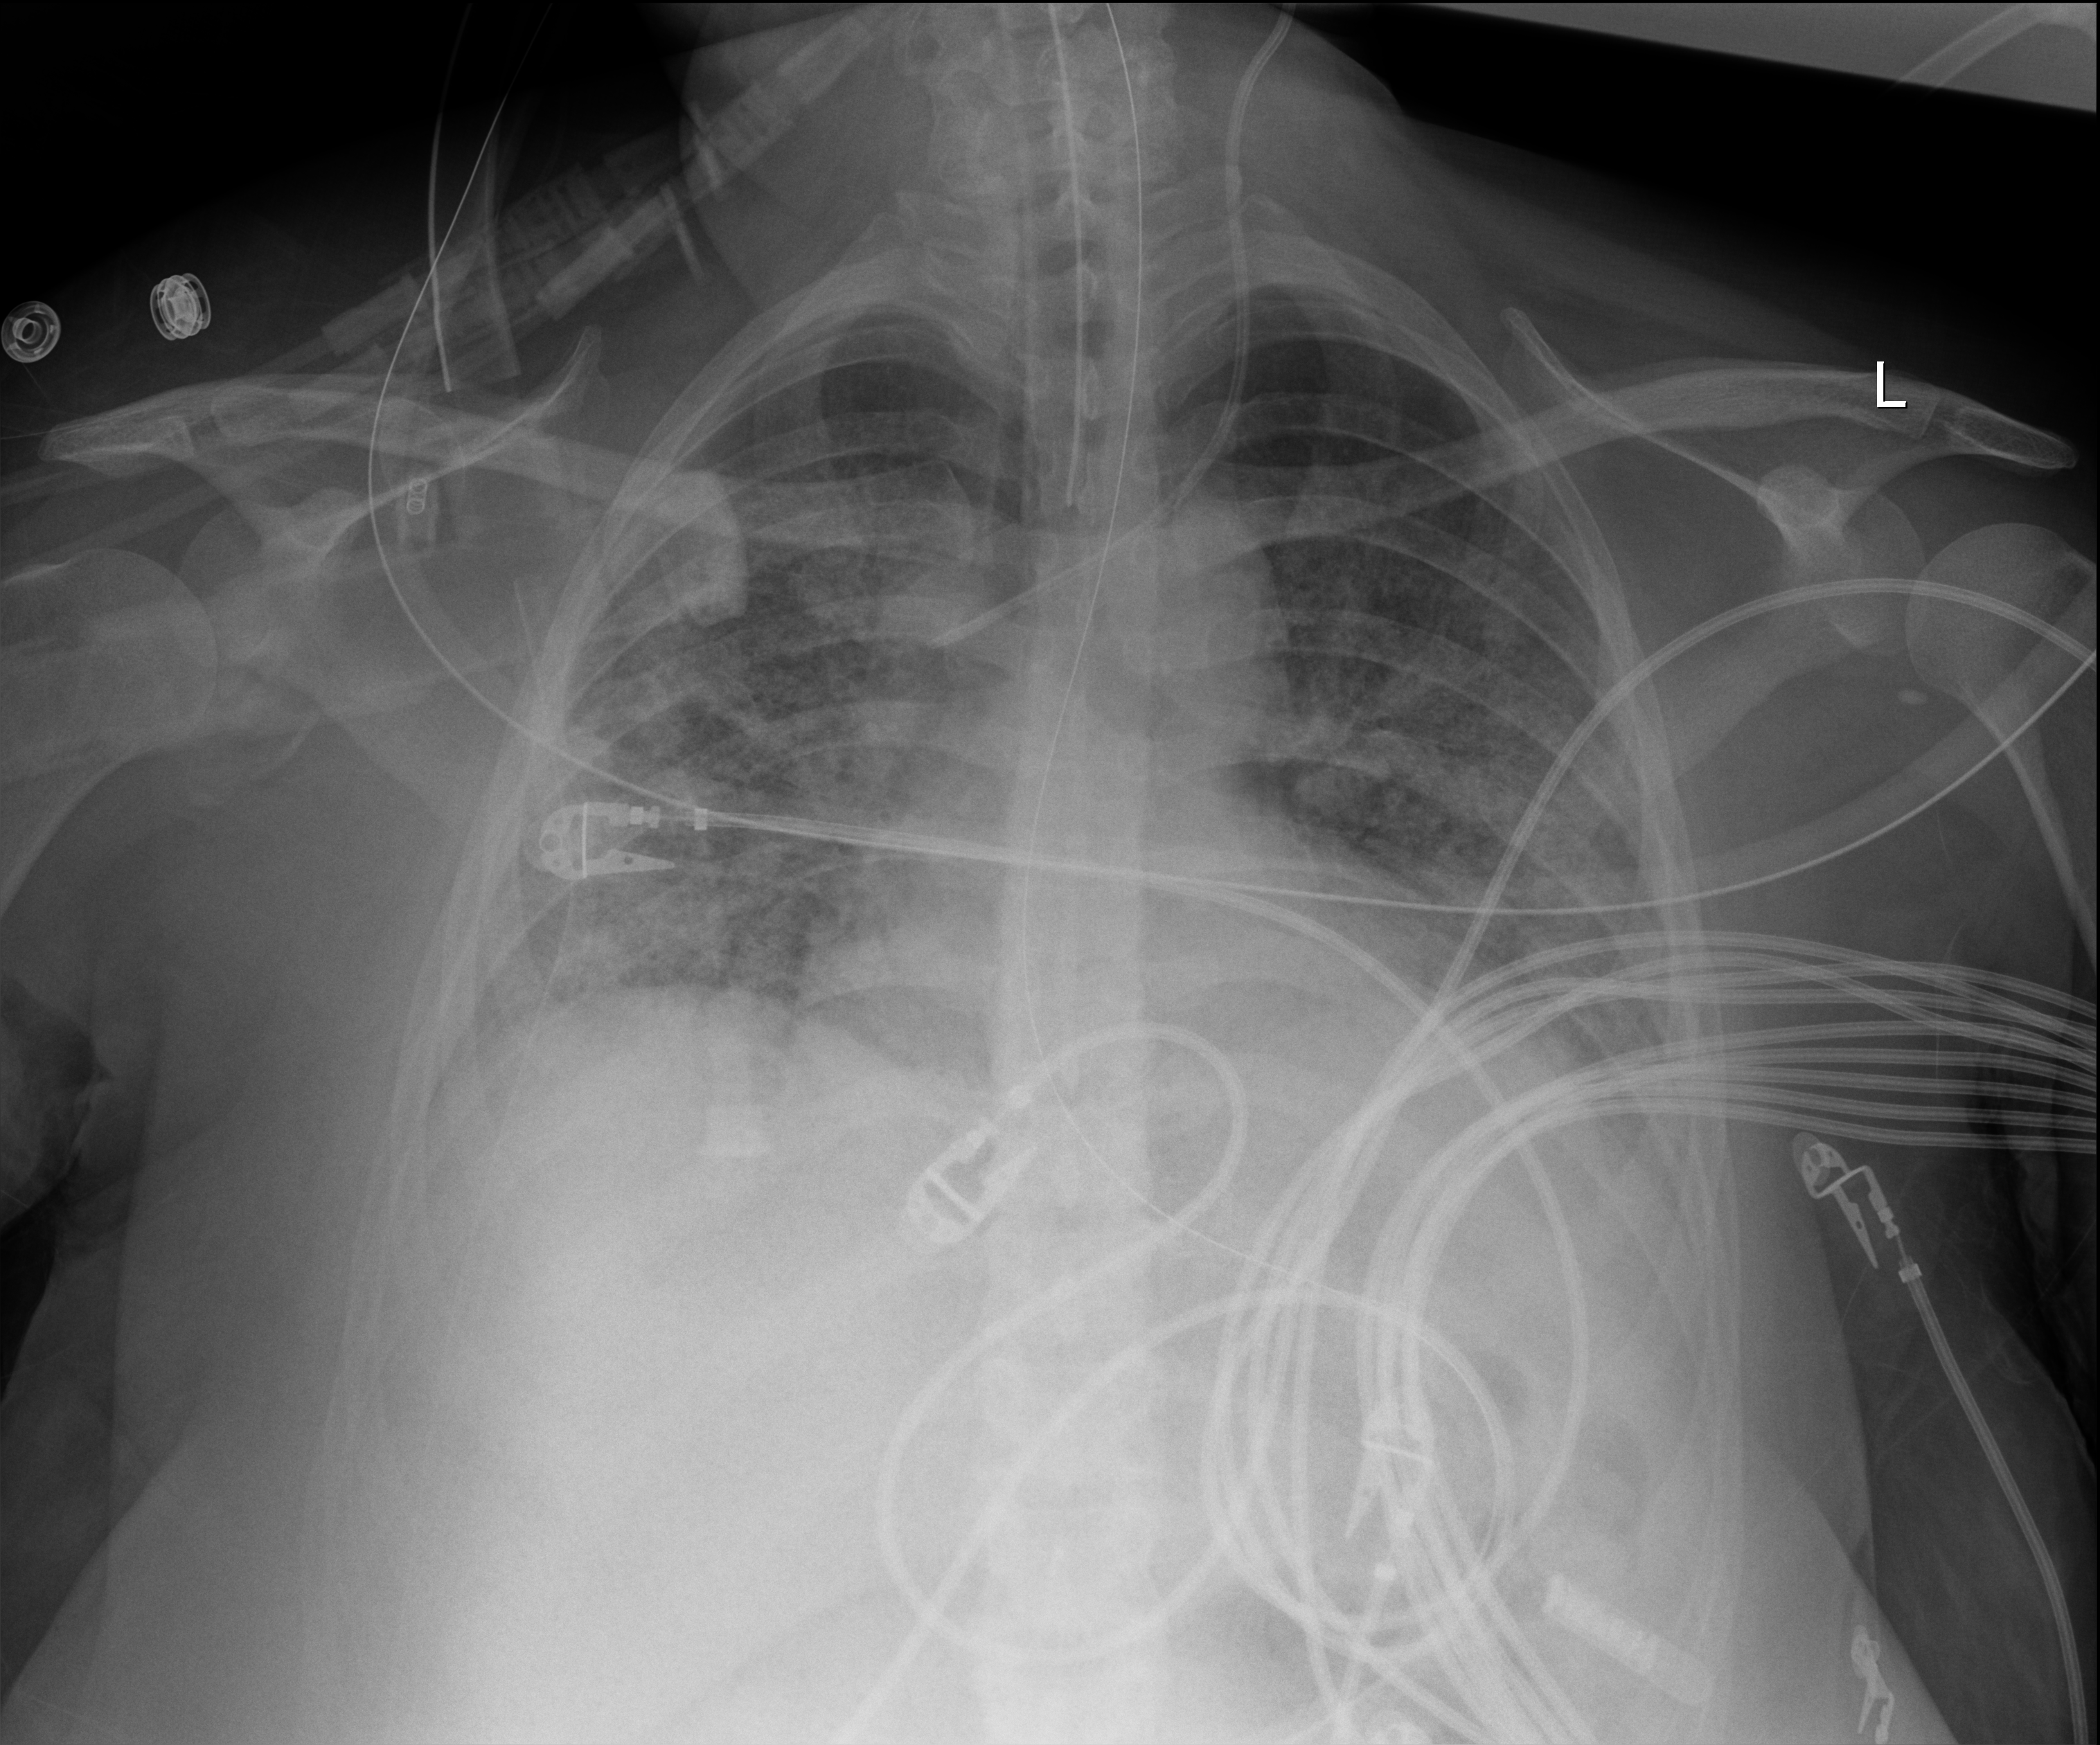
Bedside chest radiograph (digital radiography), anteroposterior (AP) projection. Patient hospitalised with COVID-19; female, aged 18–59 years.
From the hospital-stay record, not from the radiograph (when in the stay this image was taken is not recorded): mechanically ventilated during this hospital stay: yes.